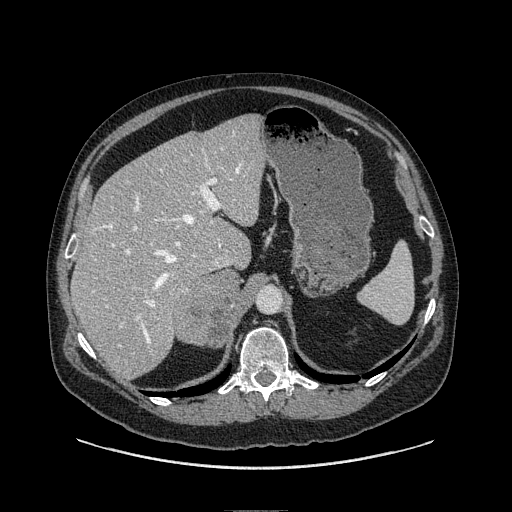
Contrast-enhanced abdominal CT, one axial slice; soft-tissue window (W 400 / L 40 HU); 1.25 mm slice thickness; 512 × 512 image matrix, field of view 440 × 440 mm. Male patient. Case-level facts recorded for this patient, not image findings: diagnosis: adrenocortical carcinoma; tumour side: right adrenal; tumour size at pathology: 7.5 cm; Ki-67 index: 15 %; stage (as recorded): 2.
Structures marked on this image (semi-automatic segmentation, software-assisted and operator-edited):
- mass: box from (x=177, y=271) to (x=263, y=344) px